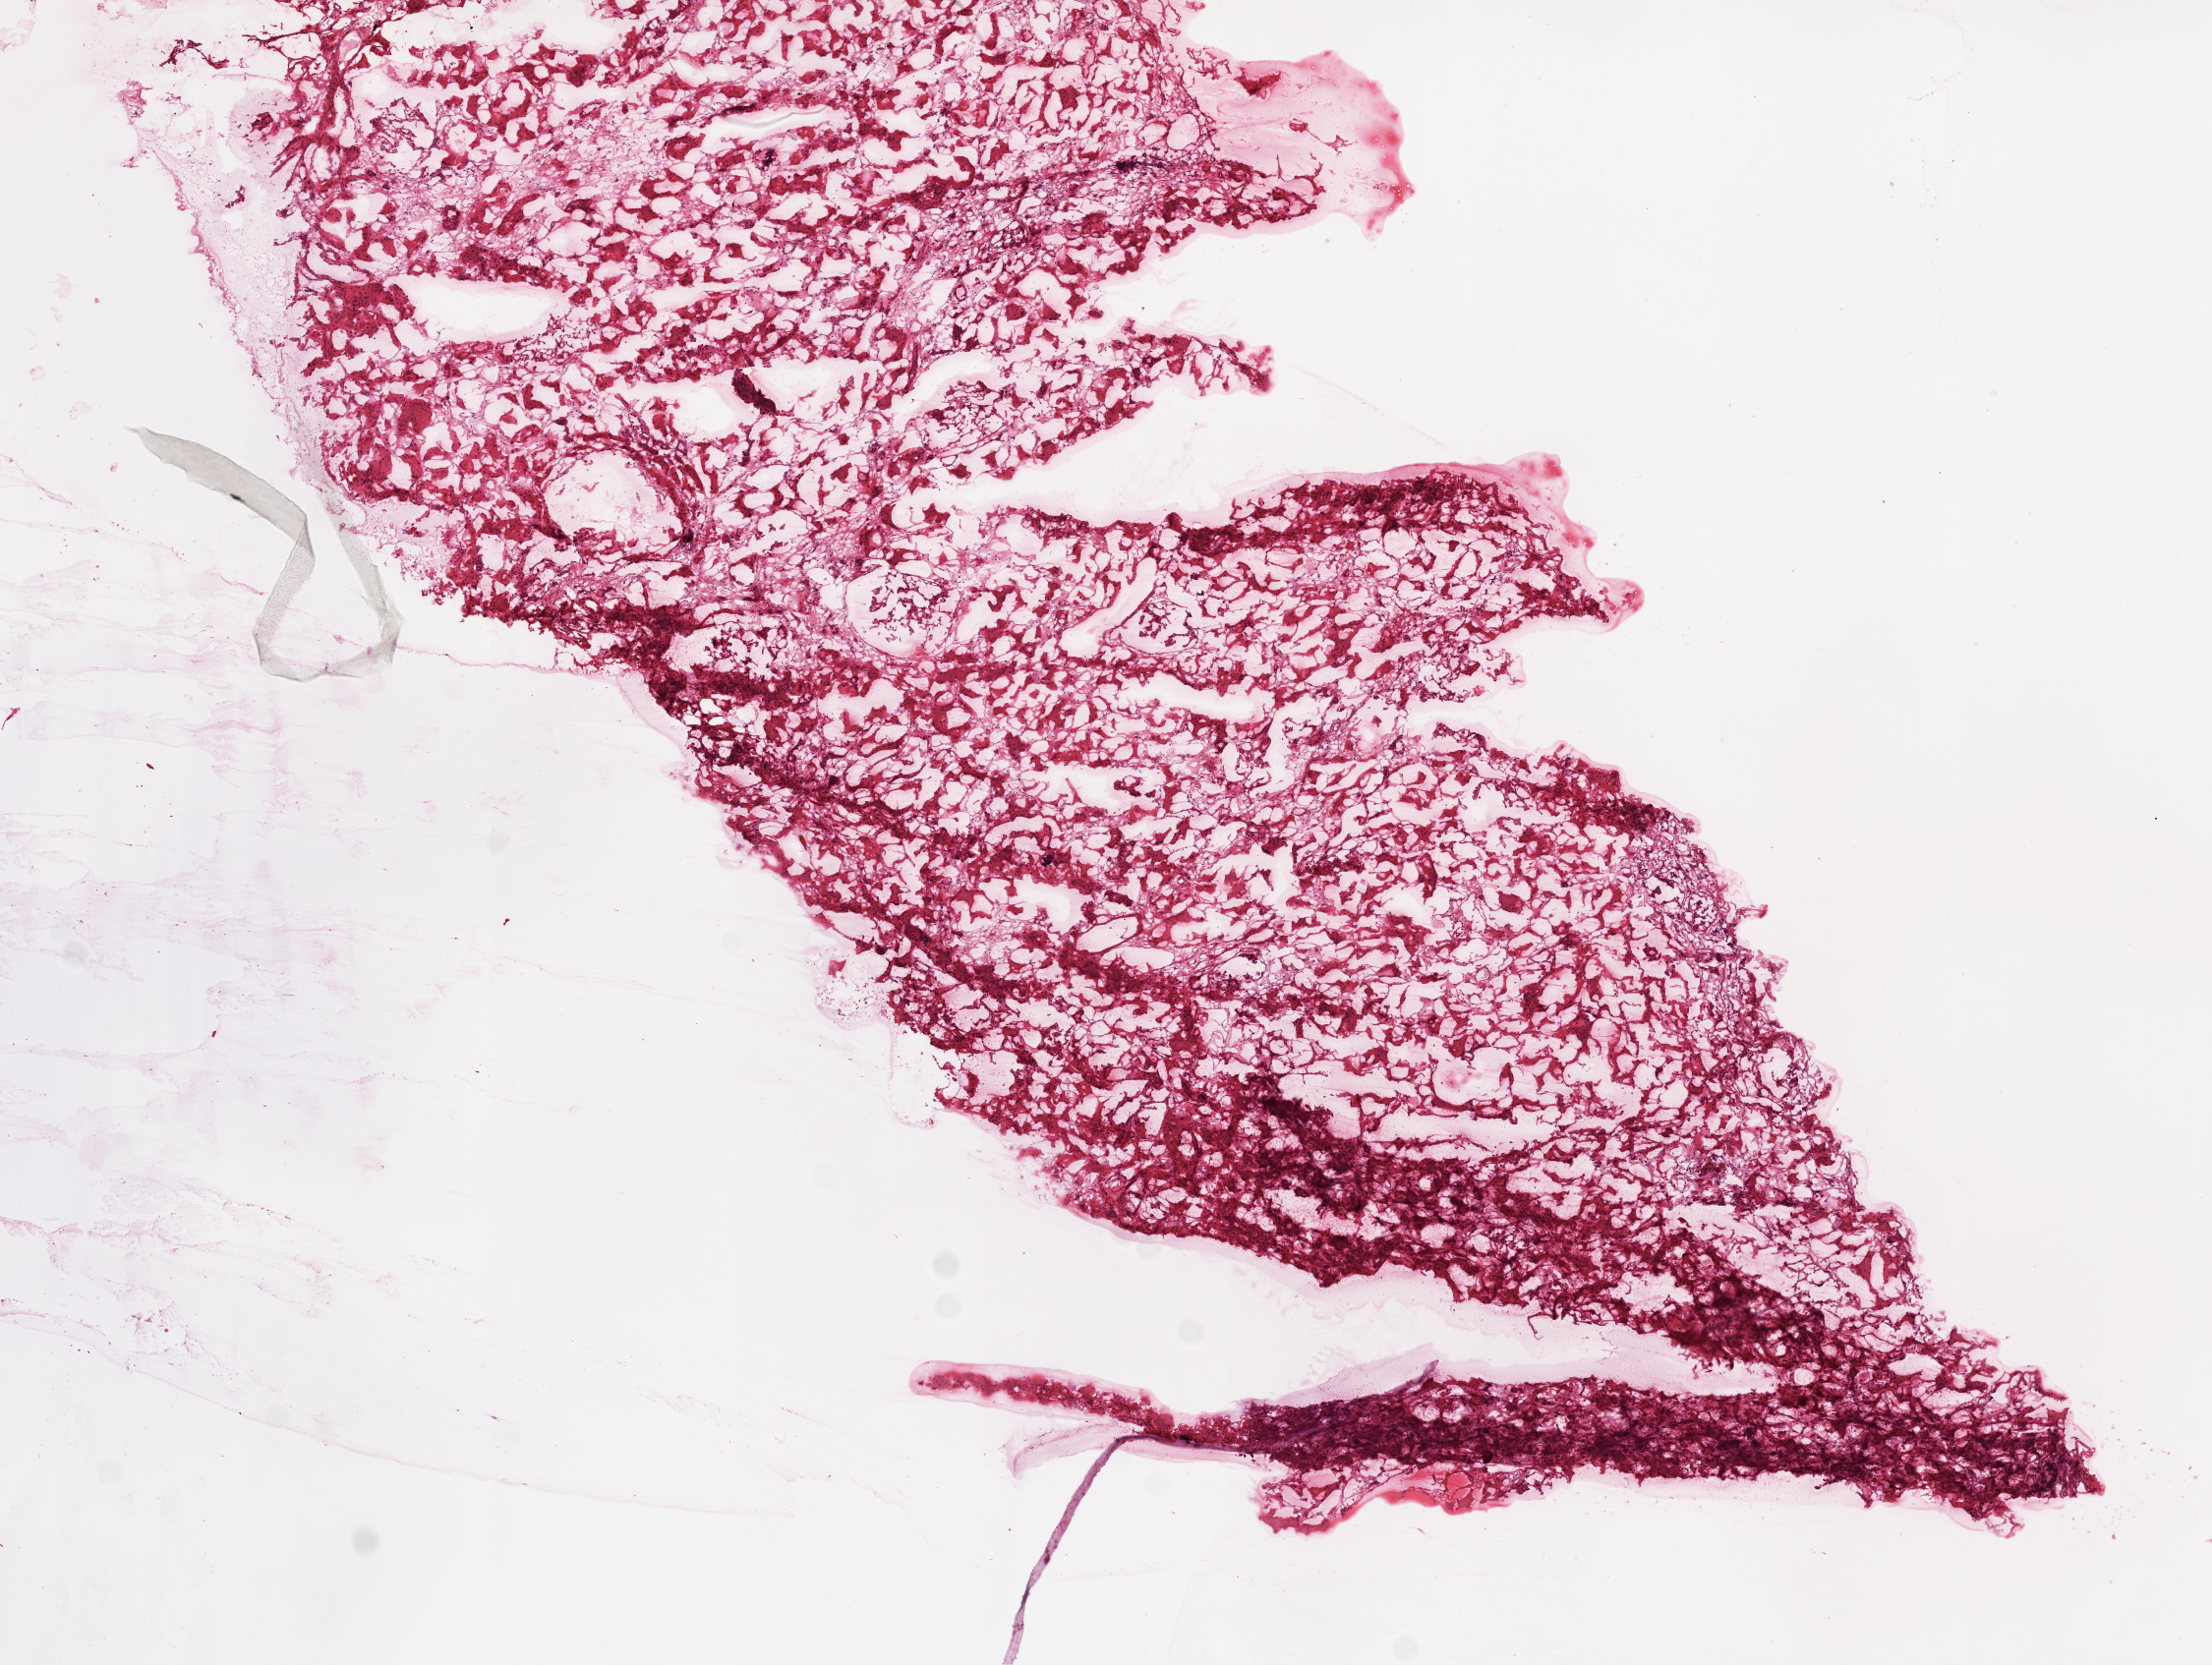
Hematoxylin and eosin (H&E) stained whole-slide image — shown as a low-resolution overview of the whole scanned area (about 9.0 x 6.8 mm). Frozen section from the top of the tissue portion. Kidney, solid tissue normal (non-tumour tissue) sample. Male, age 63 years at initial diagnosis.
This section: solid tissue normal (non-tumour) sample from the same patient. Patient diagnosis: Clear cell adenocarcinoma, NOS.